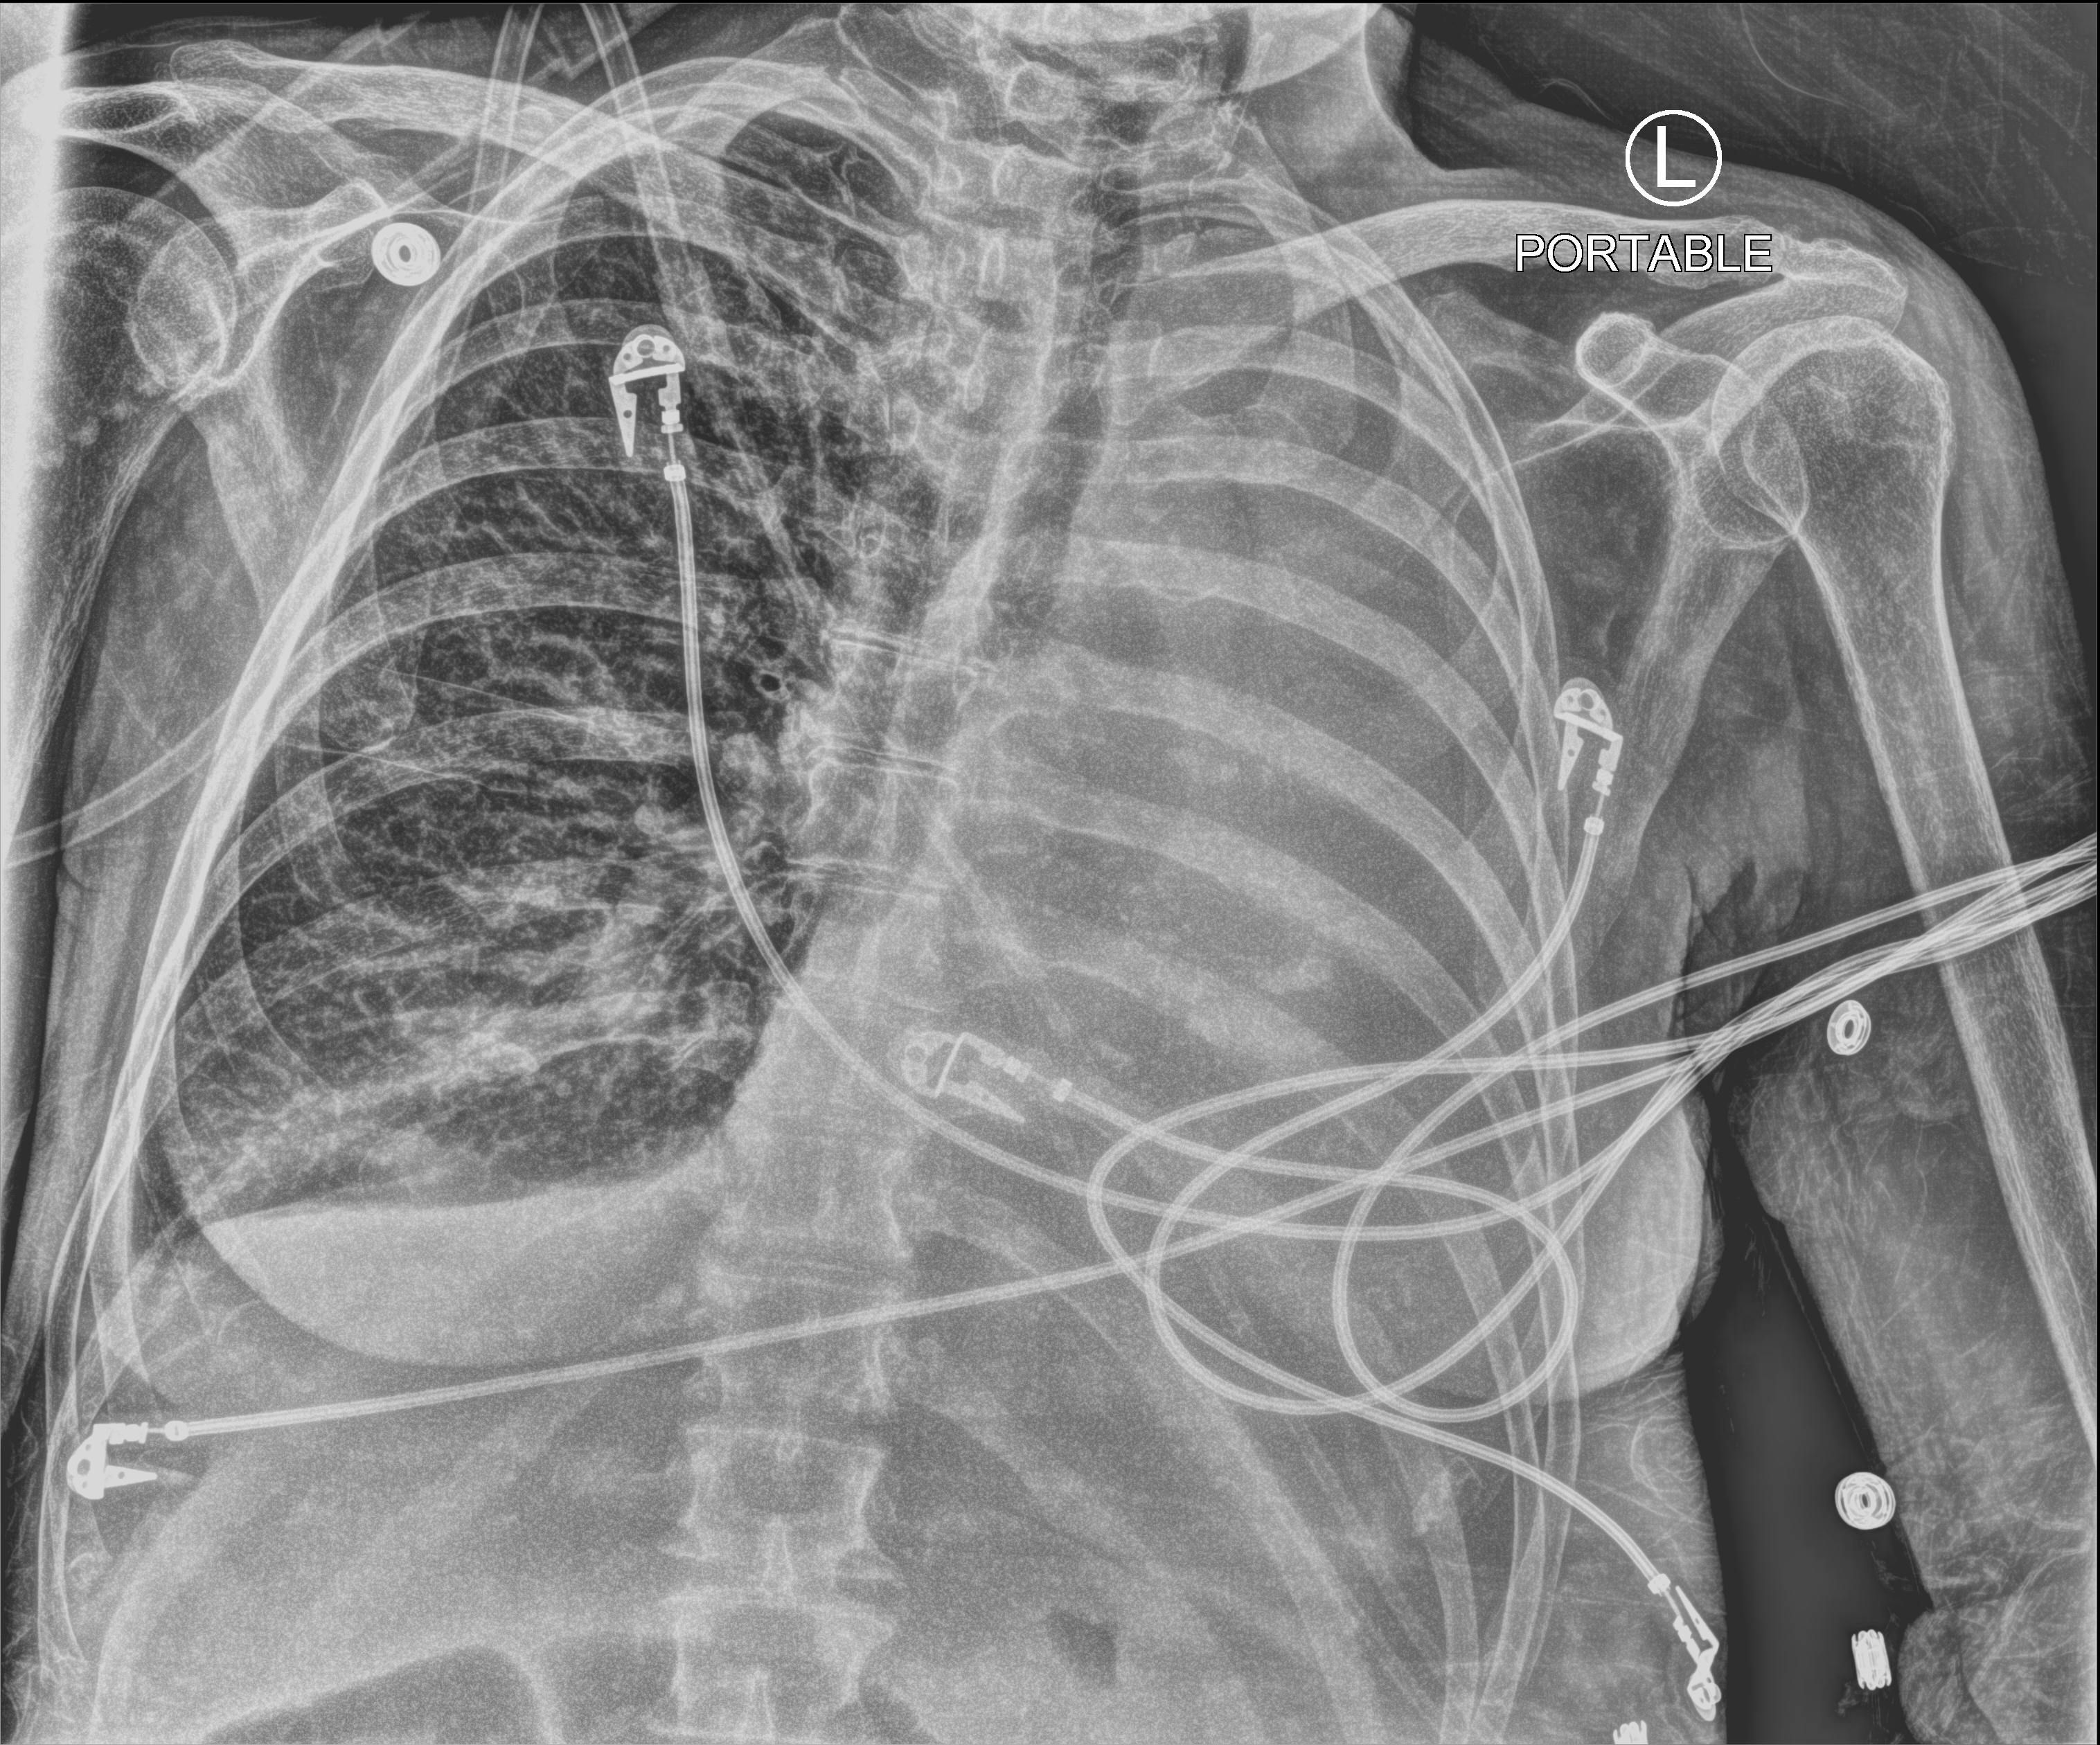
Portable chest radiograph. Female patient hospitalised with COVID-19, age 60–74 years.
From the hospital-stay record, not from the radiograph (when in the stay this image was taken is not recorded):
- mechanically ventilated during this hospital stay: yes
- admitted to intensive care during this hospital stay: yes